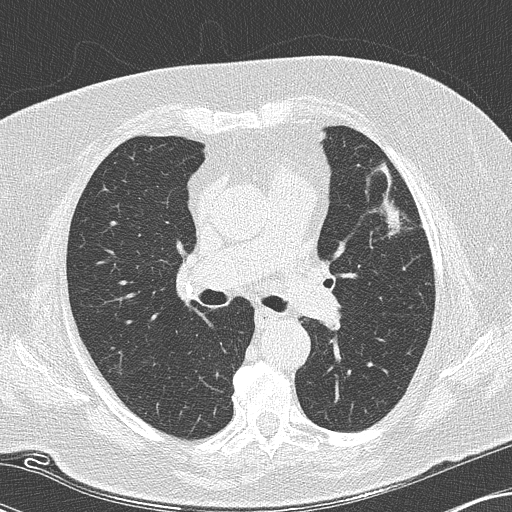
Chest CT (low-dose screening protocol), one axial image, second annual screen, lung window (W 1500 / L -600 HU), 2 mm slice thickness, slice 55 of 151 in the series, 512 × 512 image matrix. Female, age 73 years at enrolment. Current smoker at enrolment.
Lesion marked by an expert reader, bounding box [x1, y1, x2, y2] px = [359, 201, 402, 246]. The screening reader recorded 2 non-calcified nodules or masses ≥4 mm on this exam; which of them this box marks is not recorded. Participant outcome: lung cancer diagnosed 123 days after this screen — adenocarcinoma, NOS, left upper lobe, moderately differentiated (G2), stage IIIB (AJCC 6th edition), 12 mm at pathology.